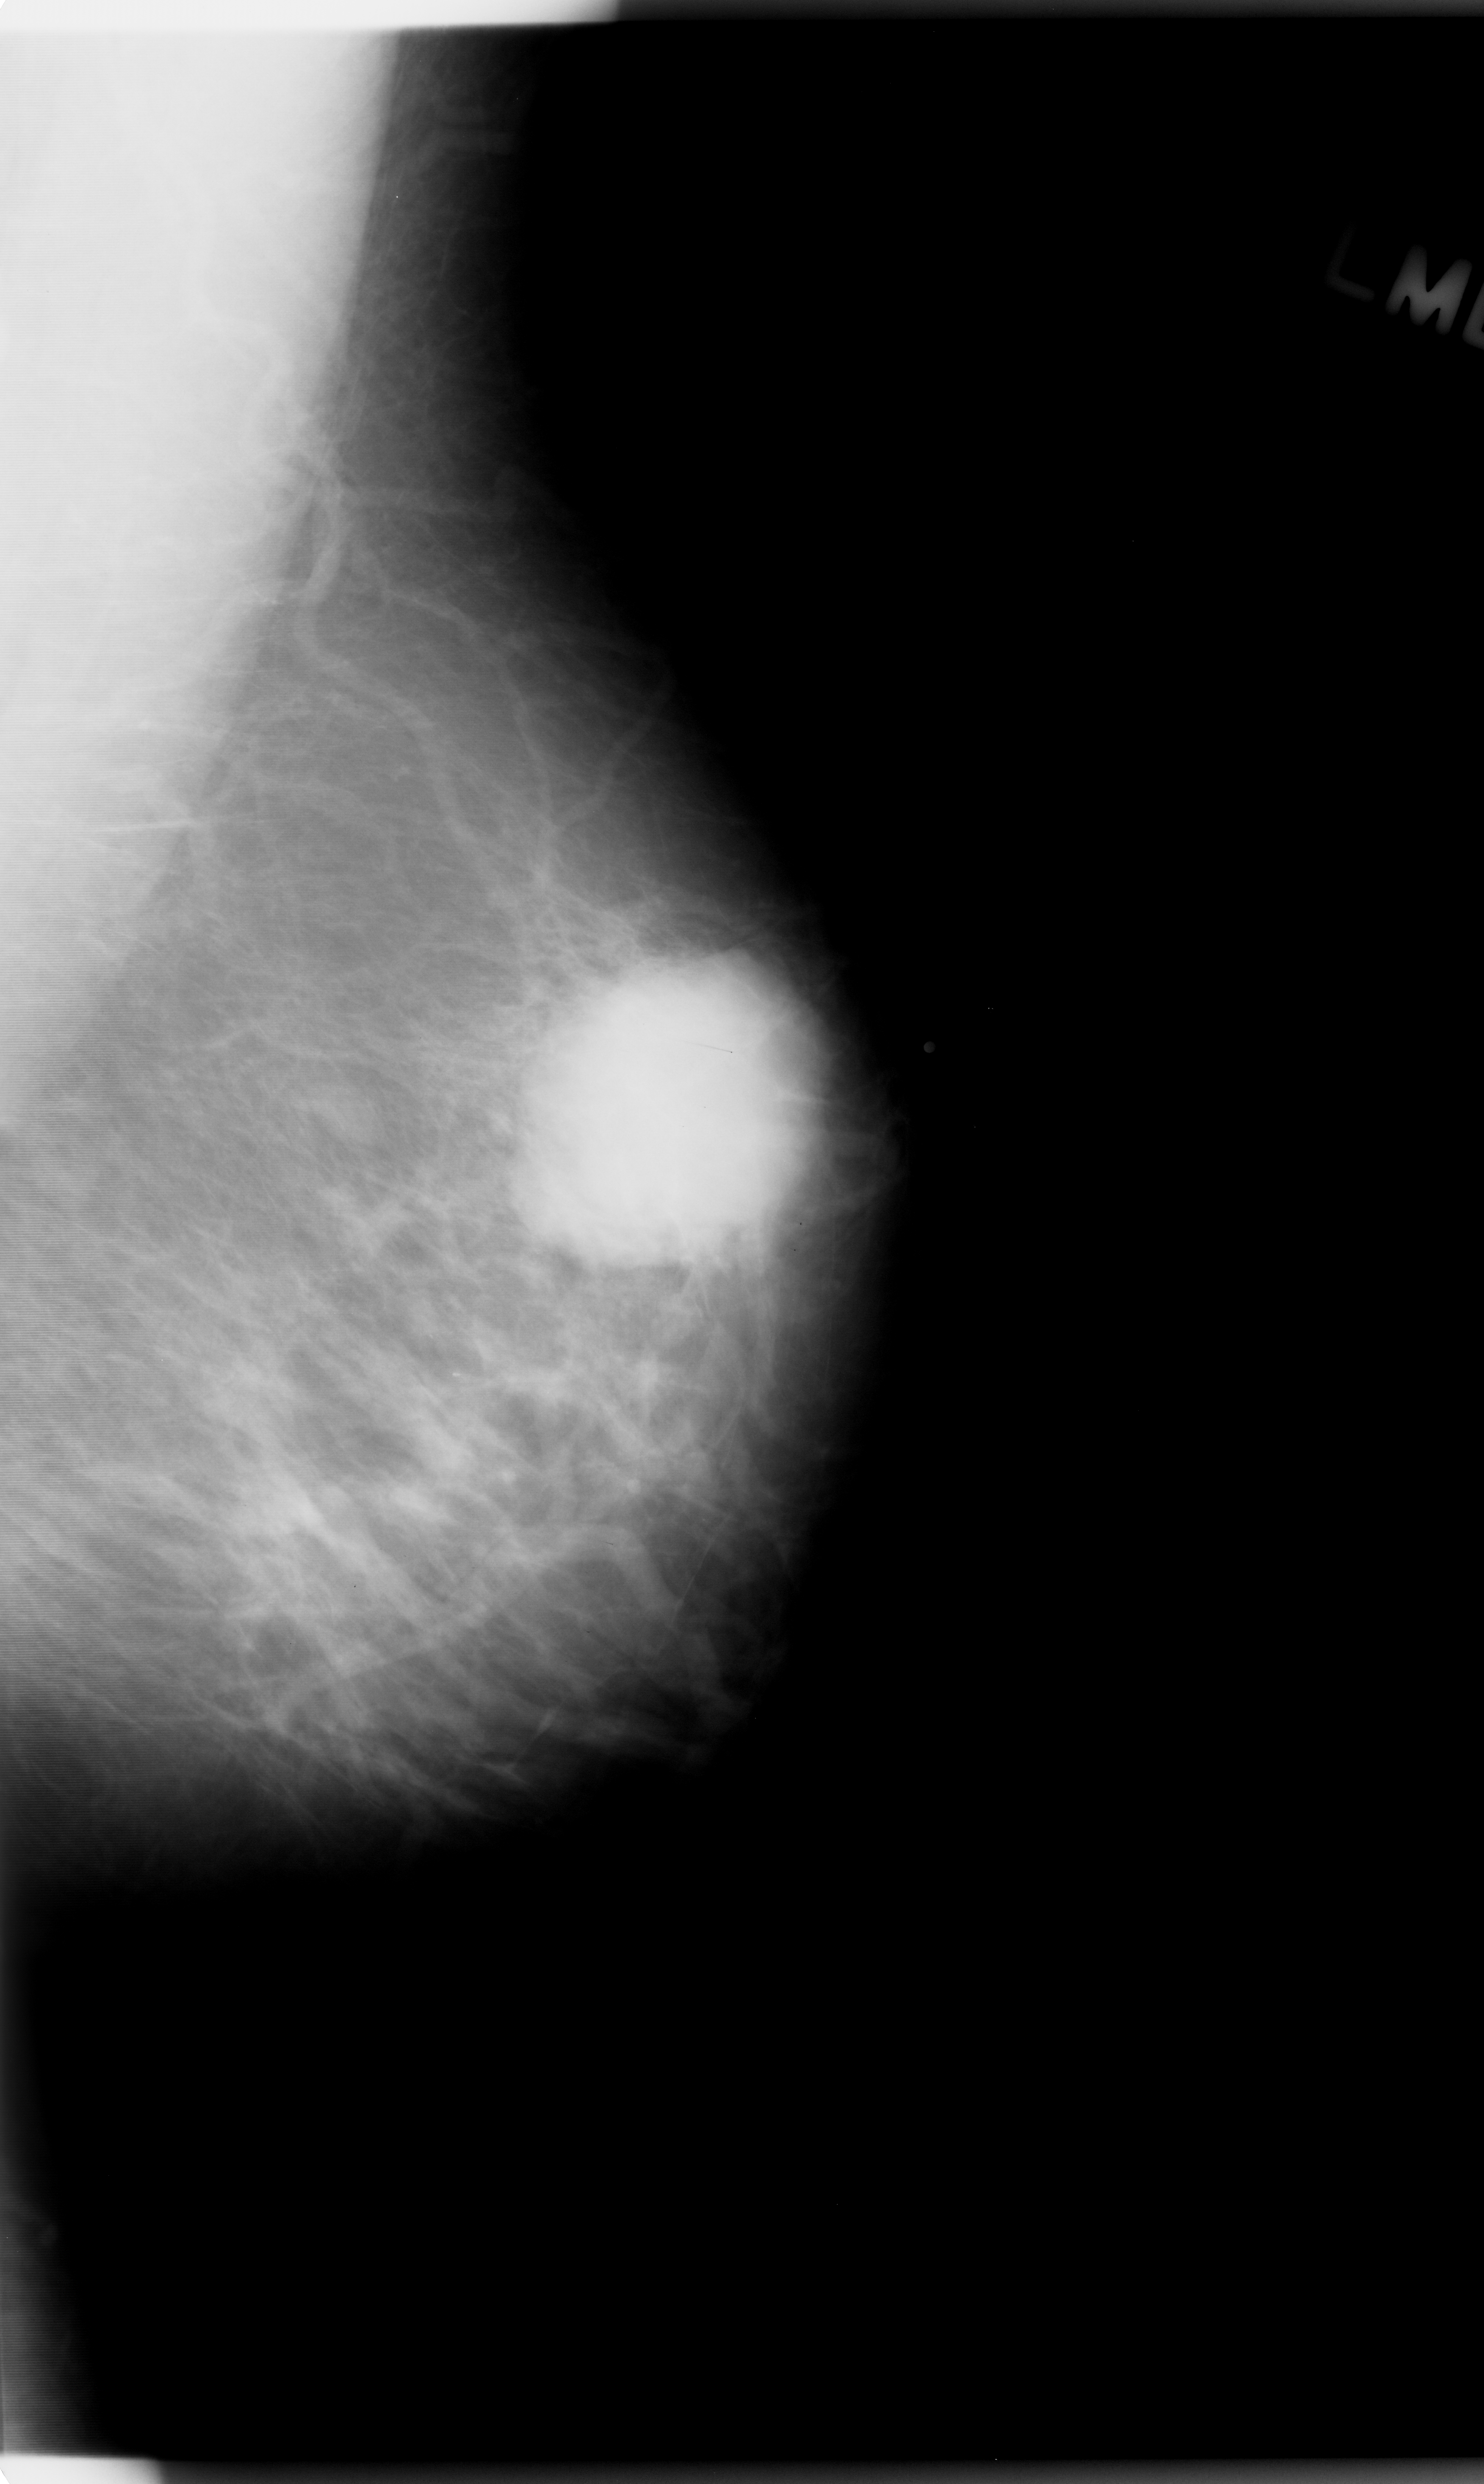
Scanned film-screen mammogram; left breast; mediolateral oblique (MLO) view.
Mass, shape oval, margins microlobulated; BI-RADS assessment category 5; pathology result (as recorded, not read from the image): malignant.